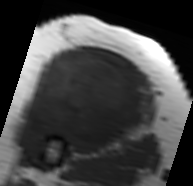
MRI of an extremity soft-tissue mass, one axial slice; slice 45 of 91 in the series (ordered by position); MR volume resampled by the dataset authors to the PET/CT grid (not the native acquisition matrix); 3.27 mm slice thickness; 193 × 186 image matrix. Female patient. From the clinical record (not read from this slice): histological type: malignant solitary fibrous tumor; grade: intermediate; site of the primary tumour: right thigh.
Annotated regions visible in this slice (expert contour drawn on MRI and transferred to this co-registered scan by the dataset authors):
- gross tumour volume including surrounding oedema: box from (x=21, y=49) to (x=150, y=148) px
- gross tumour volume (mass): (x=26, y=49)–(x=148, y=146)